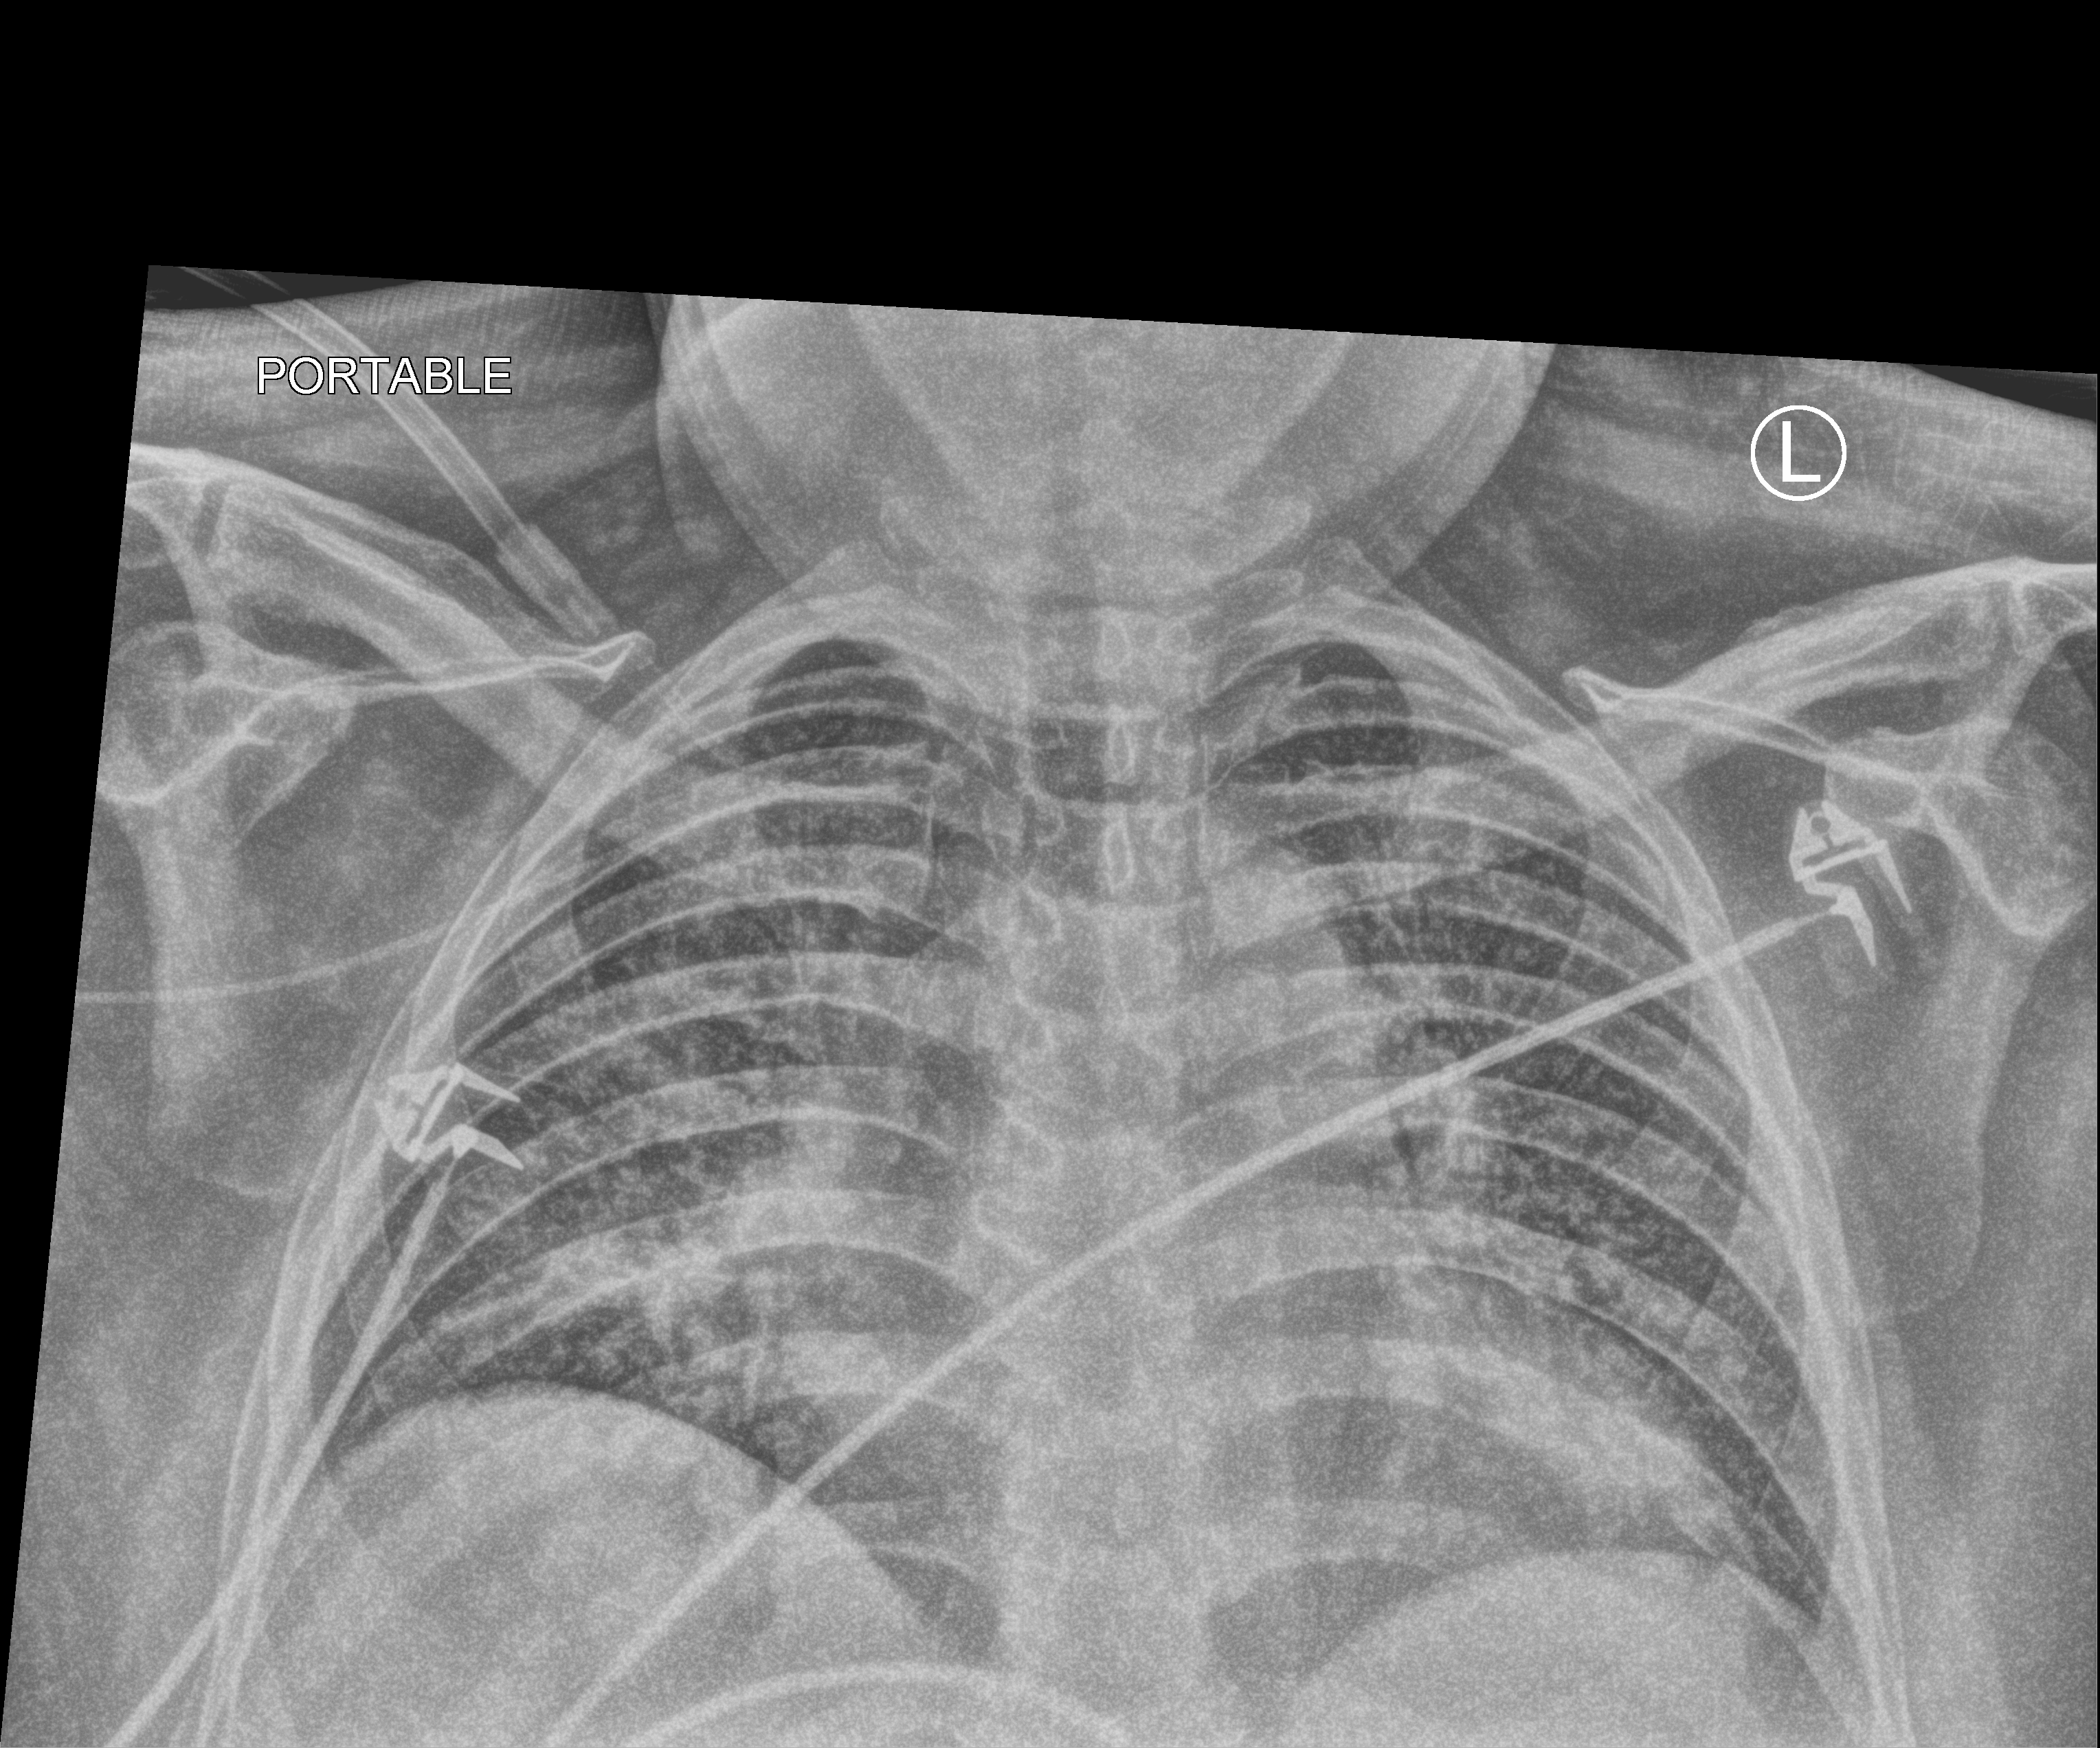
Portable chest radiograph, anteroposterior (AP) projection. Male patient hospitalised with COVID-19, age 18–59 years.
Admission-level facts for this patient (not findings on this image; timing relative to this image not recorded): mechanically ventilated during this hospital stay: yes; smoking status (admission record): never; admitted to intensive care during this hospital stay: yes.